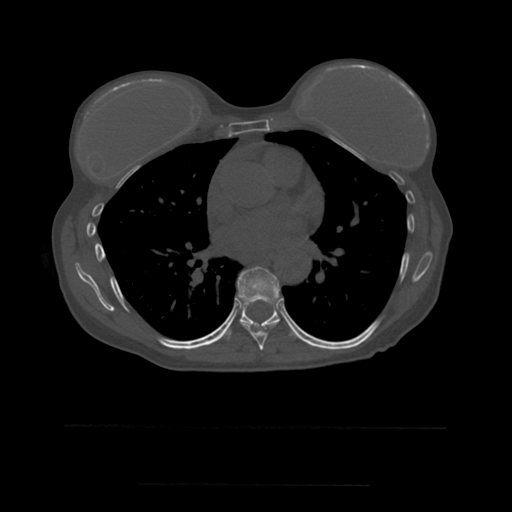
CT including the spine, one axial slice. Slice 349 of 544 in the series (ordered by position). Bone window (W 1800 / L 400 HU). 512 × 512 image matrix, field of view 350 × 350 mm. Patient age 58 years. From the clinical record (not read from this slice): primary cancer: lung.
Annotated regions visible in this slice (semi-automatically segmented with operator editing):
- T7 vertebra: bounding box [x1, y1, x2, y2] px = [237, 266, 280, 351]
- T8 vertebra: [228, 293, 281, 339]